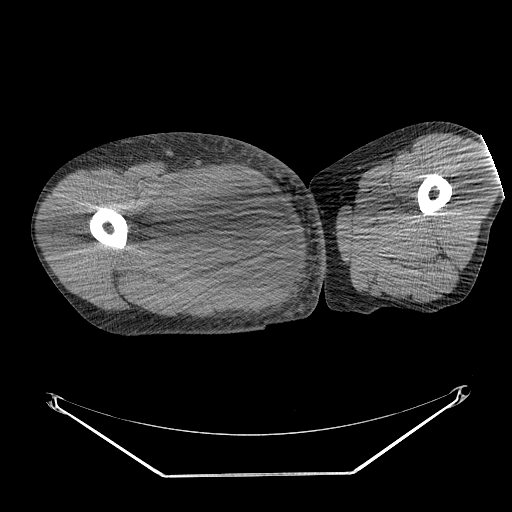
CT of an extremity soft-tissue mass (from a PET/CT study), one axial slice; slice 253 of 311 in the series (ordered by position); soft-tissue window (W 400 / L 40 HU); 3.75 mm slice thickness; 512 × 512 image matrix, field of view 500 × 500 mm. Male patient. Case-level facts recorded for this patient, not image findings: histological type: undifferentiated - pleiomorphic; grade: high; site of the primary tumour: right thigh.
Structures marked on this image (expert contour drawn on MRI and transferred to this co-registered scan by the dataset authors):
- gross tumour volume including surrounding oedema: box from (x=137, y=171) to (x=261, y=270) px
- gross tumour volume (mass): (x=155, y=173)–(x=259, y=268)